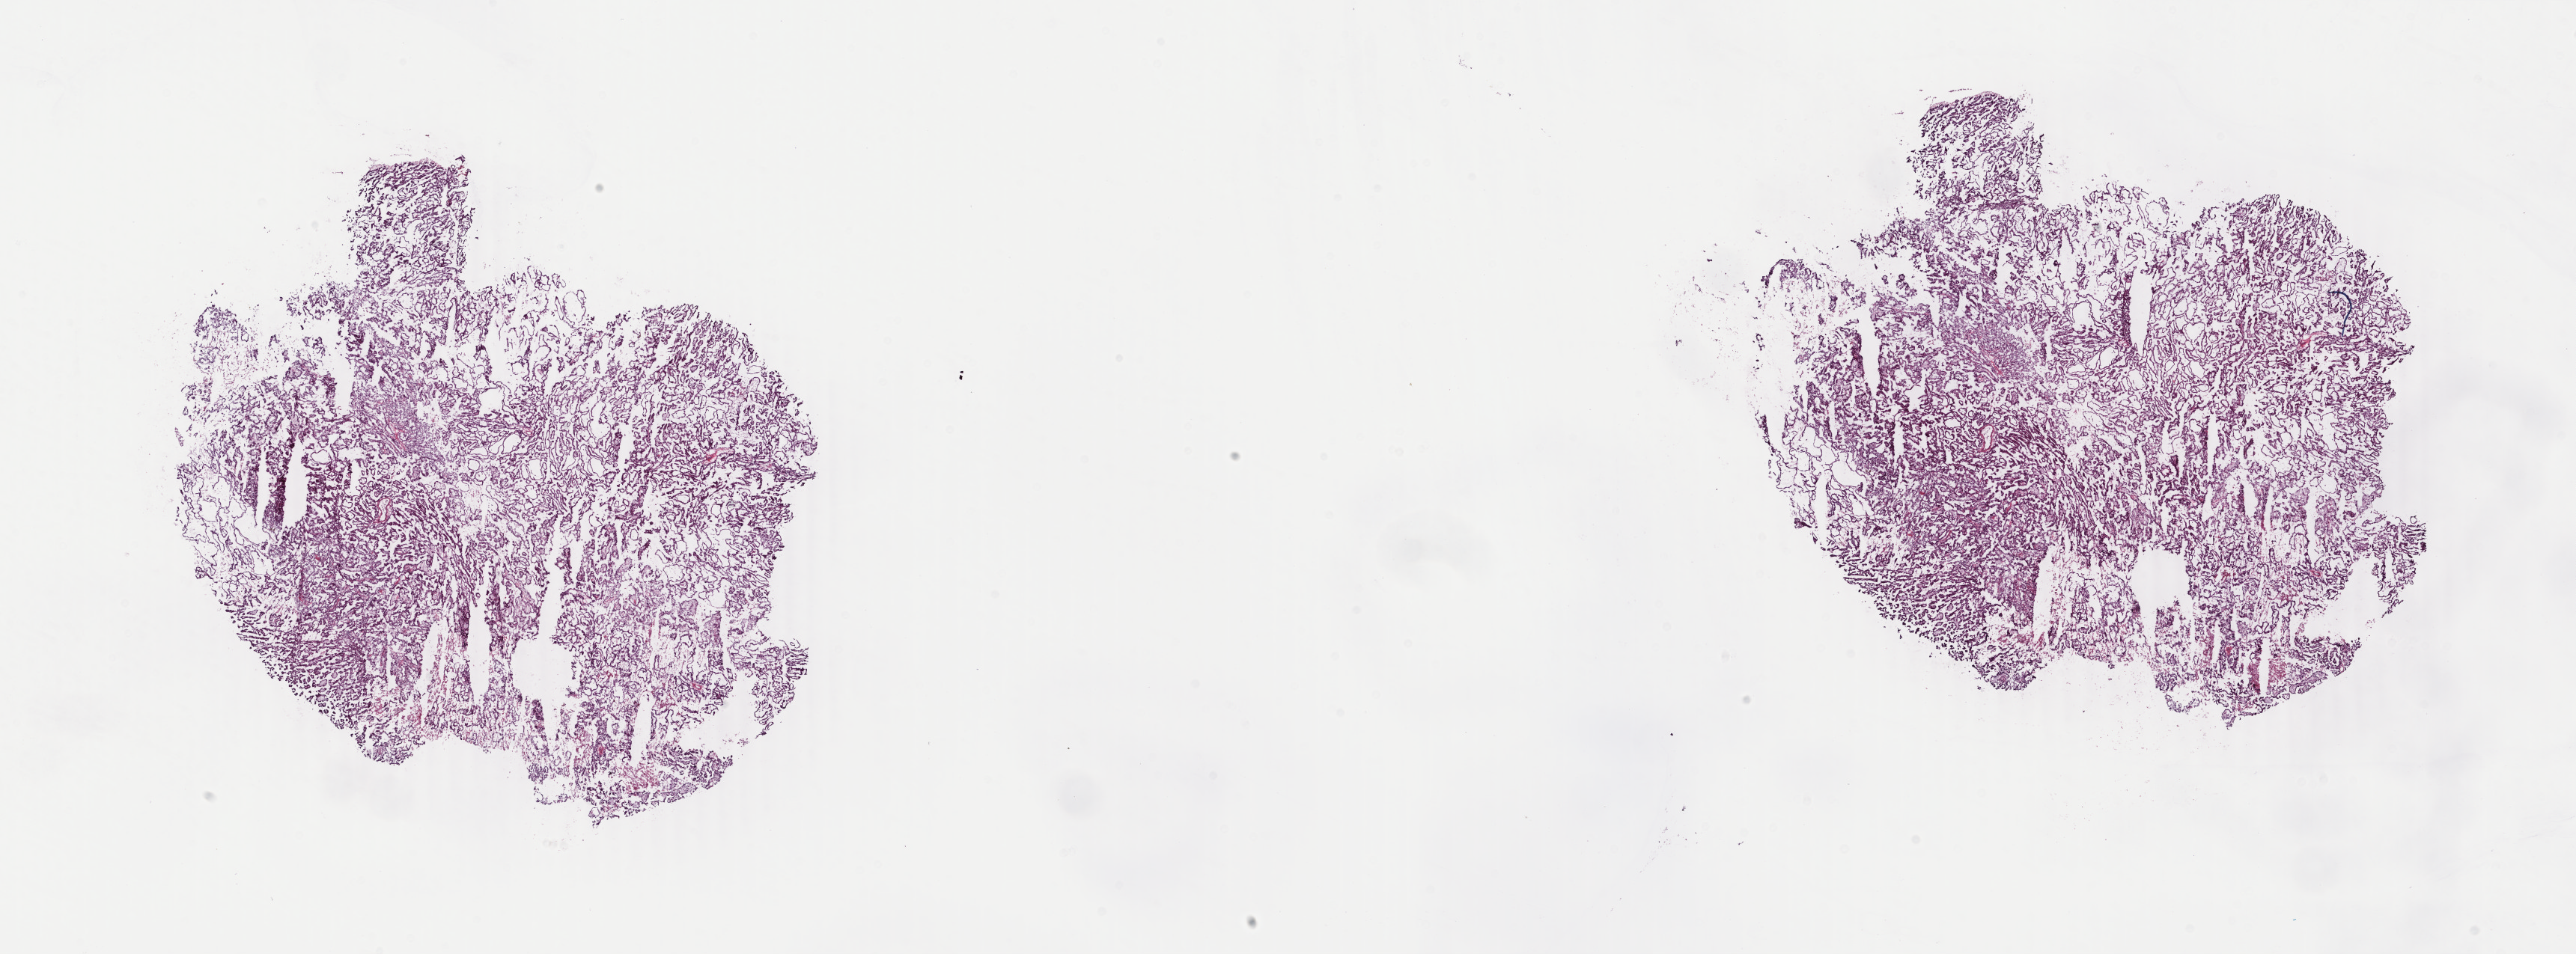
Whole-slide histology image, Hematoxylin and eosin (H&E) stained, a low-resolution overview of the entire scanned area, about 27.4 x 10.1 mm. Frozen section. Kidney, primary tumour sample. Patient: male, age at initial diagnosis 73 years. Composition of this section per pathologist review: tumour cells 100%, tumour nuclei 80%, normal cells 0%, stromal cells 0%, necrosis 0%. Inflammatory infiltration, as recorded: lymphocyte infiltration 2%, monocyte infiltration 3%, neutrophil infiltration 0%.
* diagnosis: Papillary adenocarcinoma, NOS
* laterality: left
* AJCC pathologic stage: I (7th edition)